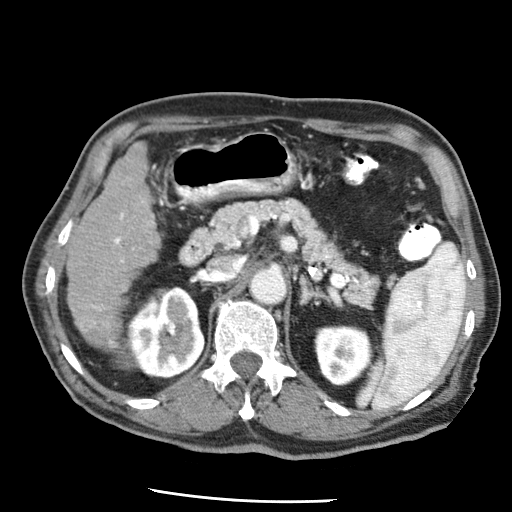
Contrast-enhanced abdominal CT (liver protocol), one axial slice. Slice 21 of 79 in the series (ordered by position). Reconstruction kernel STANDARD. Soft-tissue window (W 400 / L 40 HU). 2.5 mm slice thickness. 512 × 512 image matrix. From the clinical record (not read from this slice): diagnosis: hepatocellular carcinoma (patient treated with transarterial chemoembolisation; whether this scan precedes or follows treatment is not stated here); TNM stage (as recorded): Stage-IIIA; Child-Pugh class: A; tumour differentiation: moderately differentiated; tumour nodularity: multinodular.
Outlined on this slice (semi-automatically segmented with operator editing):
- liver parenchyma outside the tumour (the mass and vessels are separate outlines, so this box may not span the whole liver): bounding box <66,142,160,346> (left, top, right, bottom; pixels)
- liver vessels: <93,213,124,343>